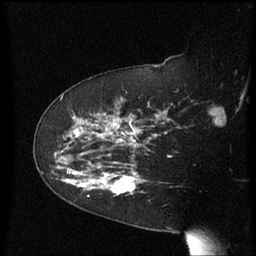
Breast MRI (dynamic contrast-enhanced), one sagittal slice. Position 42 of 60 along the scan axis. Dynamic contrast-enhanced series, image 2 of 3 at this slice position (ordered by acquisition). 1.5 T. TE 4.2 ms, TR 8.4 ms. 2.3 mm slice thickness. 256 × 256 image matrix. Patient: female, 63 years. Case-level facts recorded for this patient, not image findings: setting: breast cancer imaged before/during neoadjuvant chemotherapy; receptor status: HER2-positive.
Outlined on this slice (semi-automatic segmentation, software-assisted and operator-edited):
- analysis volume of interest (the breast-tissue region the enhancement analysis was run in; not a lesion): bounding box [x1, y1, x2, y2] px = [63, 144, 147, 206]
- tumour enhancement mask (voxels above the 70 % enhancement threshold inside the analysis volume of interest): [63, 144, 141, 194]